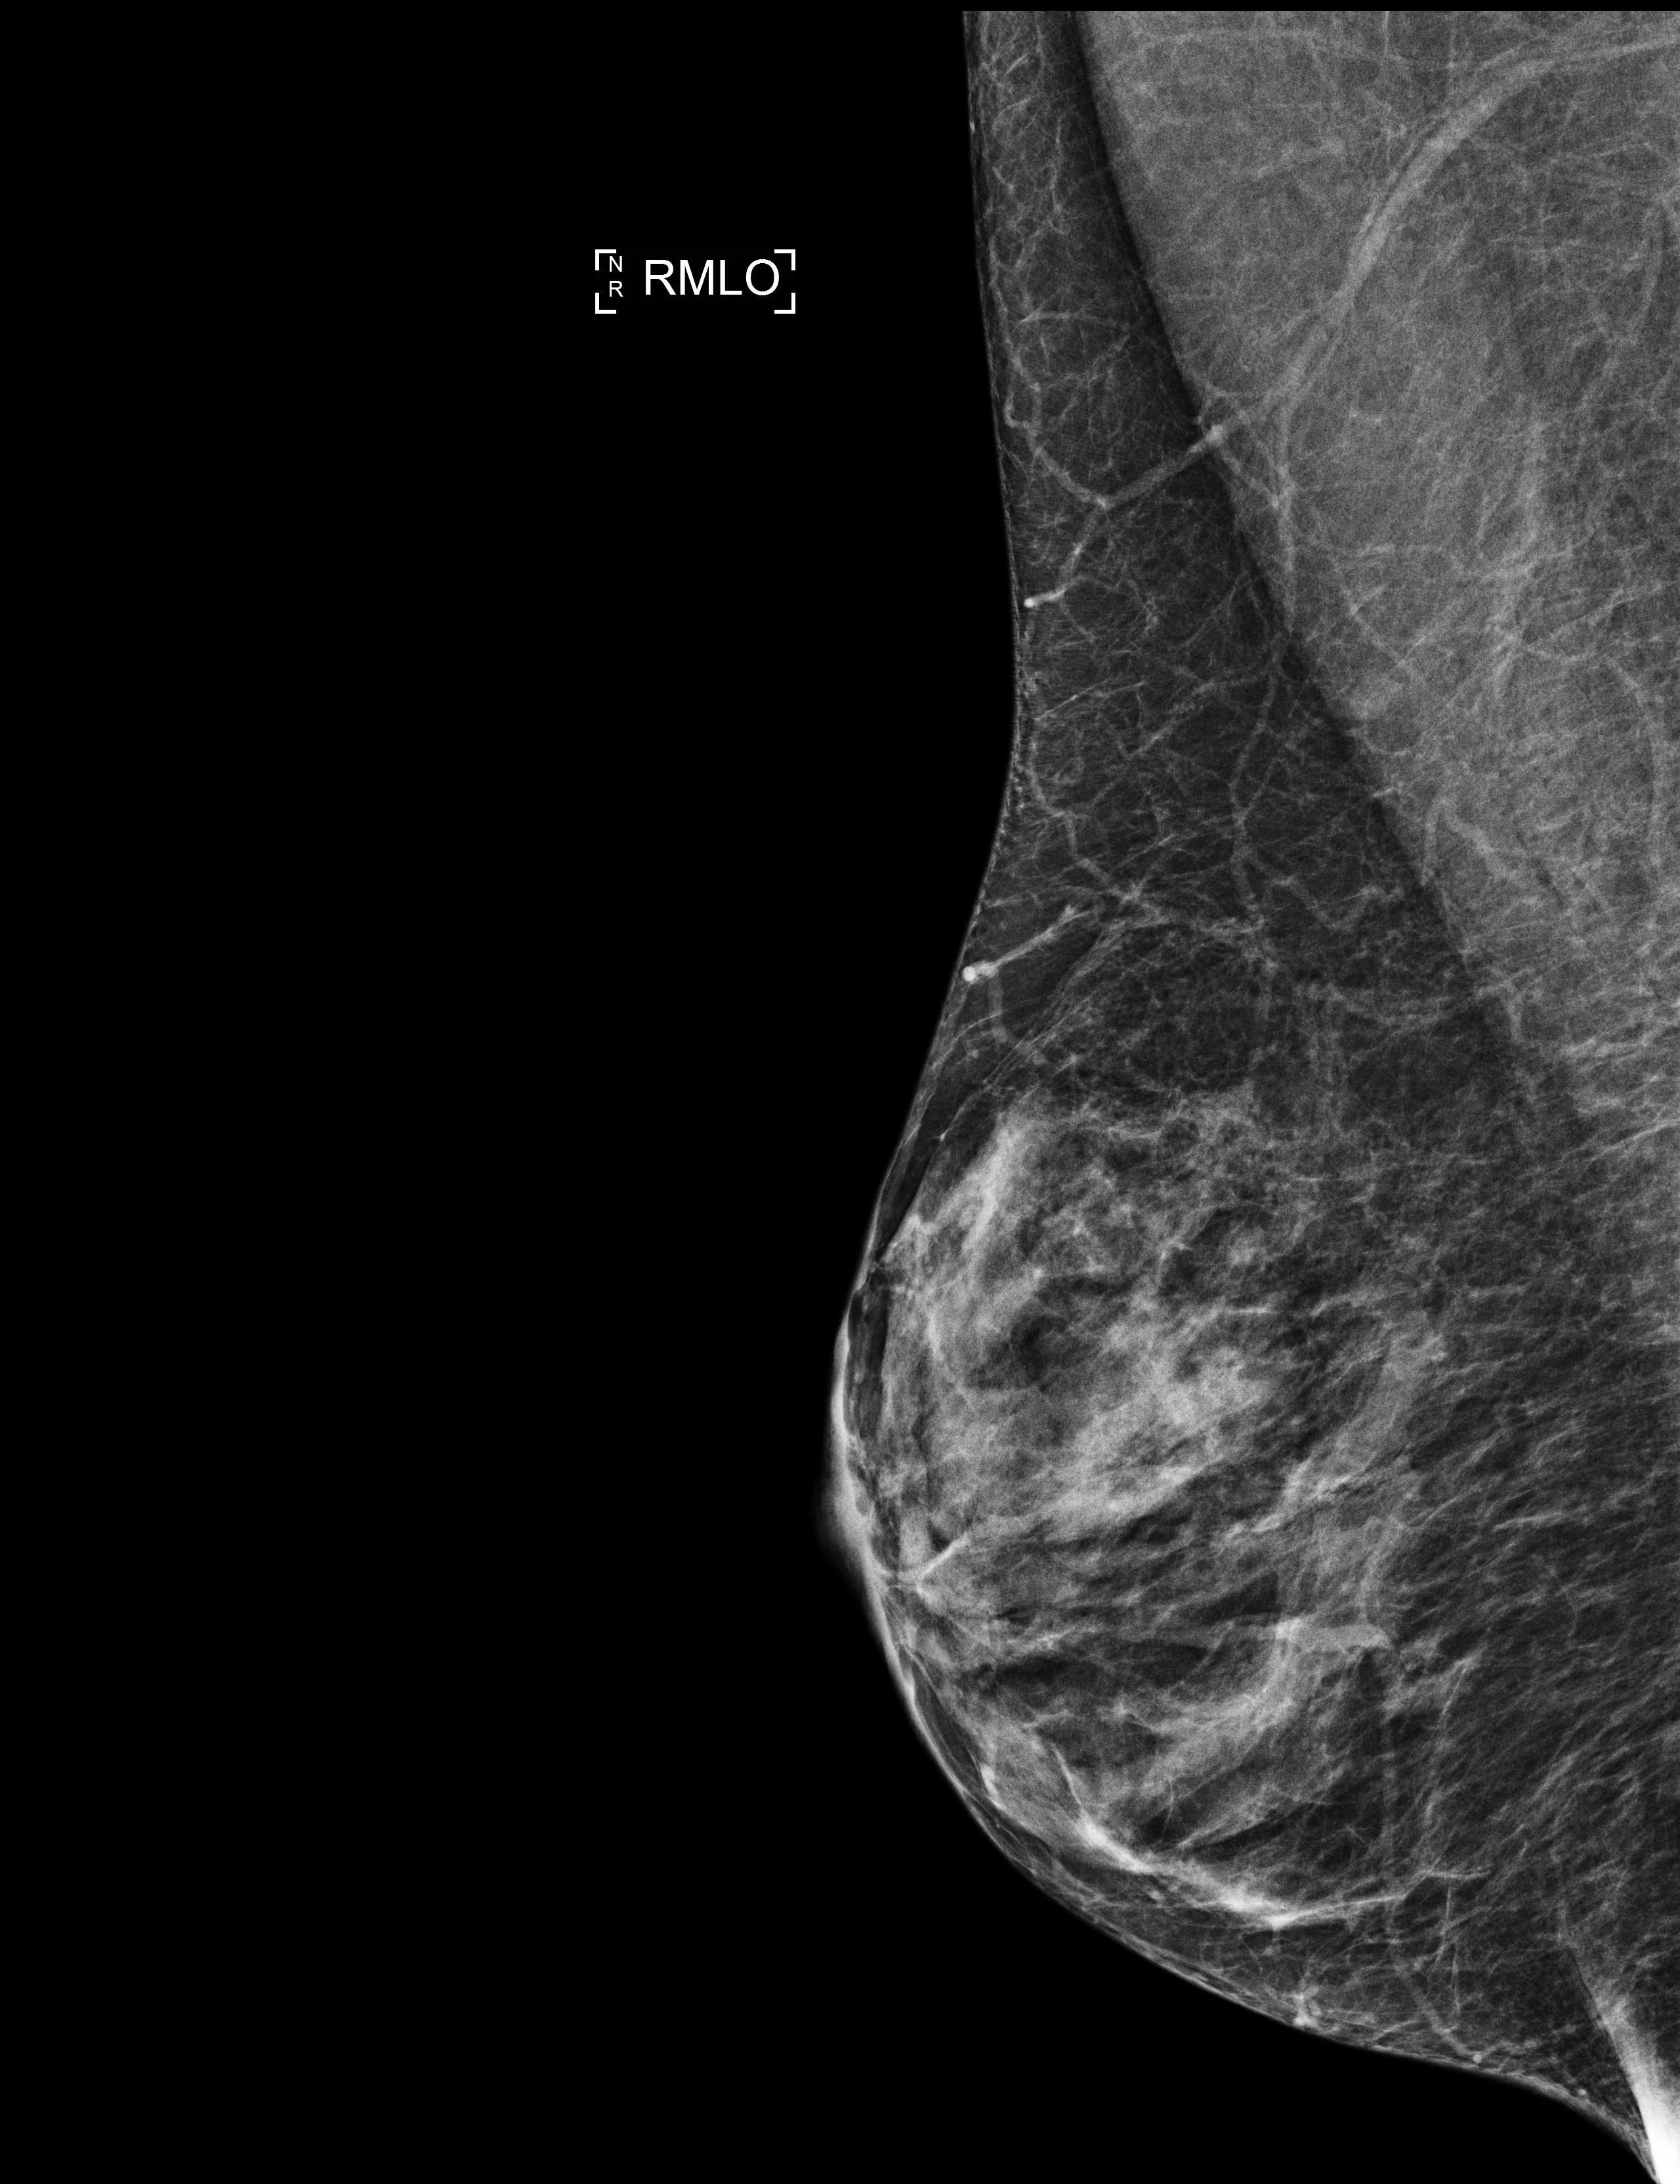
Digital mammogram (FFDM); right breast; mediolateral oblique (MLO) view; screening examination. Patient aged 59 years (female).
- BI-RADS breast density category at the screening exam (both breasts, scale 1–4): 2
- final BI-RADS assessment for this screening round (tomosynthesis exam, both breasts): category 1
- recall: no recall after this screen